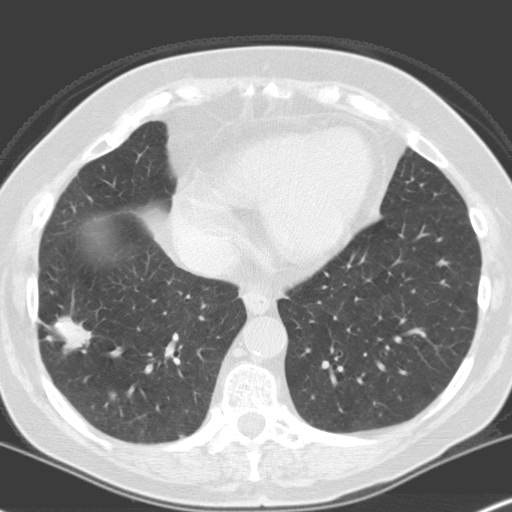
Axial slice from a low-dose chest CT screening exam, baseline annual screen, lung window (W 1500 / L -600 HU), 3.2 mm slice thickness, slice 99 of 160 in the series. Female, age 70 years at enrolment. Current smoker at enrolment.
- Expert reader's lesion annotation, bounding box (x1, y1, x2, y2) in pixels: (30, 296, 100, 365).
- The screening reader recorded 4 non-calcified nodules or masses ≥4 mm on this exam (right lower lobe, right upper lobe, left upper lobe, left upper lobe); which of them this box marks is not recorded.
- Official screen result: positive, change unspecified: nodule(s) >= 4 mm or enlarging nodule(s), mass(es), or other non-specific abnormalities suspicious for lung cancer.
- Participant outcome: lung cancer diagnosed 28 days after this screen — adenocarcinoma, NOS, right lower lobe, moderately differentiated (G2), stage IV (AJCC 6th edition), 28 mm at pathology.